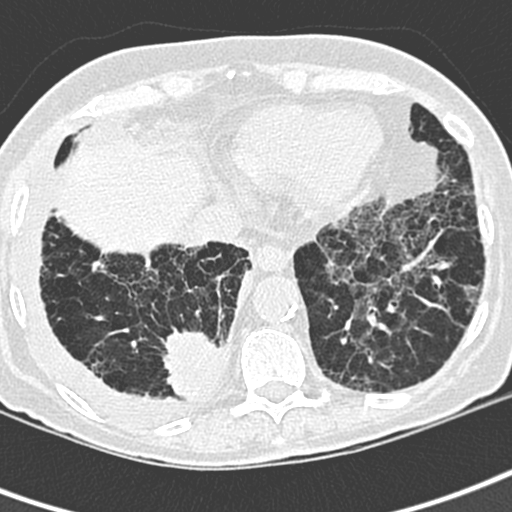
Low-dose screening chest CT, one axial slice. Position 75 of 220 along the scan axis. Lung window (W 1500 / L -600 HU). 512 × 512 image matrix, field of view 288 × 288 mm.
Outlined on this slice (manually delineated by an expert):
- lesion 1 (tumor, lower lobe of right lung): bounding box [x1, y1, x2, y2] px = [163, 330, 222, 398]